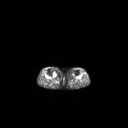
FDG PET of an extremity soft-tissue mass (from a PET/CT study), one axial slice; slice 154 of 267 in the series (ordered by position); 3.27 mm slice thickness; 128 × 128 image matrix. Patient: female, 65 years. From the clinical record (not read from this slice): histological type: undifferentiated – high grade; grade: high; site of the primary tumour: right thigh.
Outlined on this slice (expert contour drawn on MRI and transferred to this co-registered scan by the dataset authors):
- gross tumour volume (mass): box from (x=53, y=72) to (x=57, y=77) px